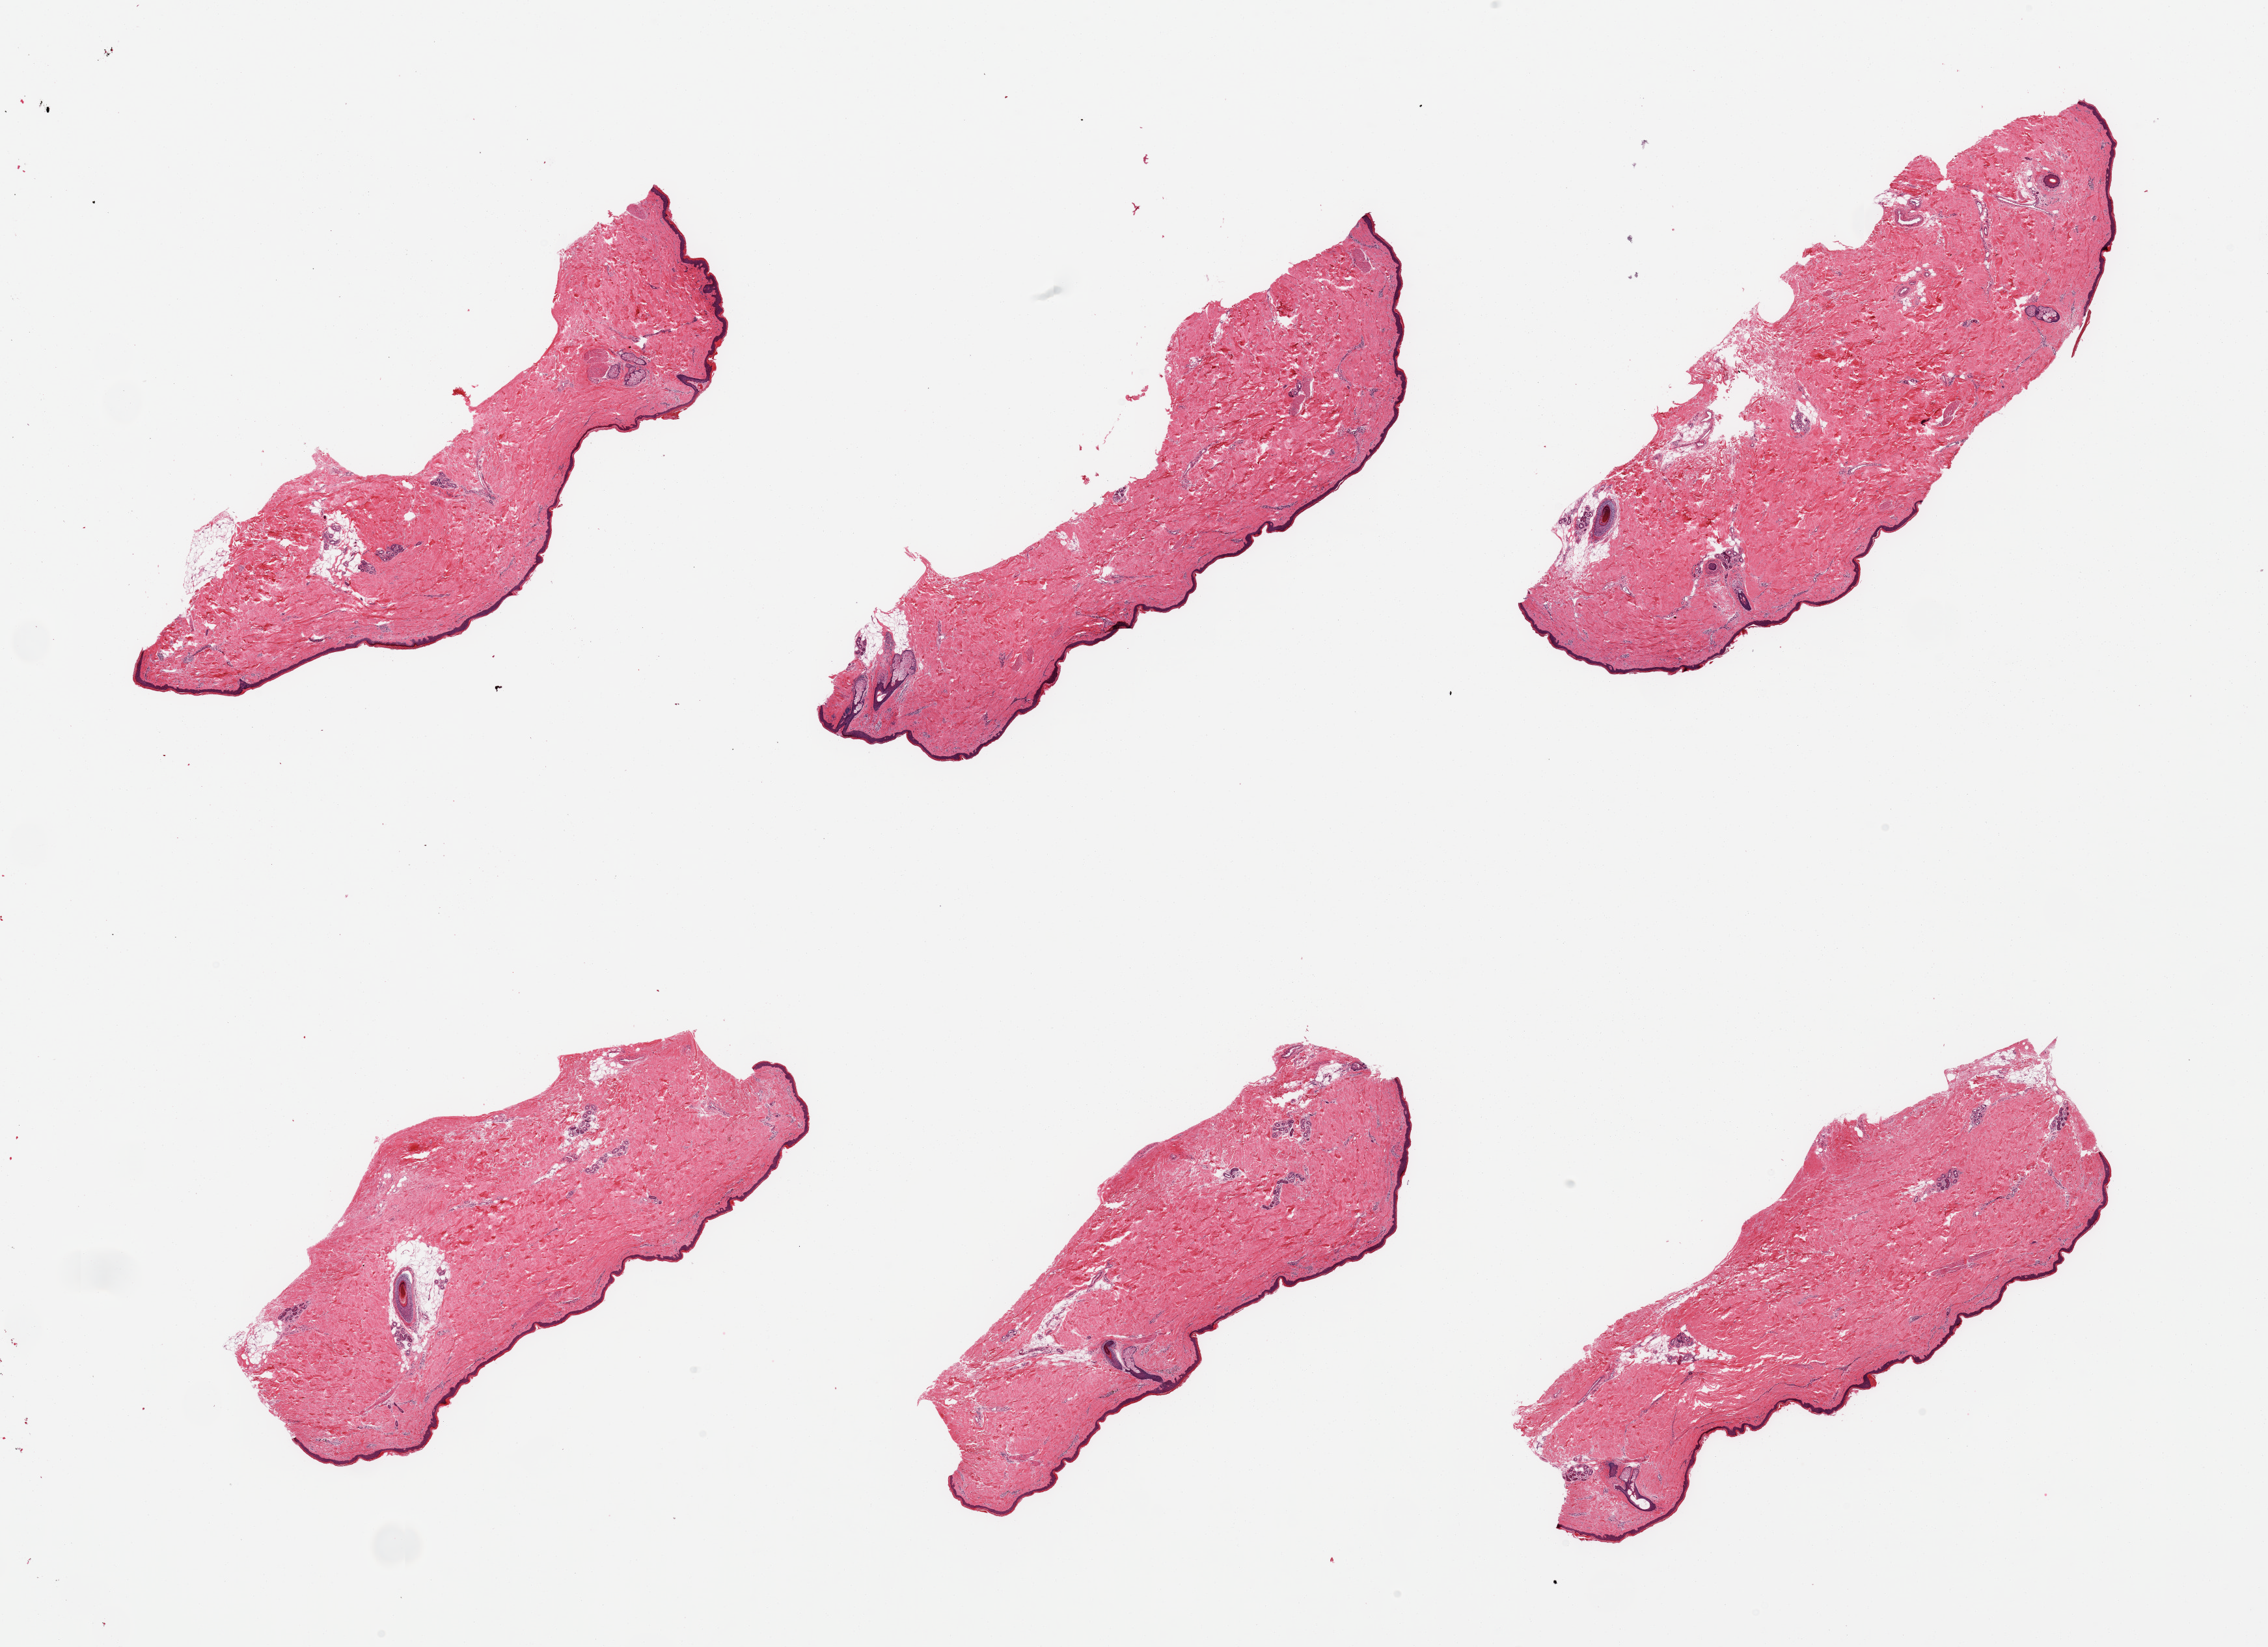
Whole-slide image, H&E stain, whole scanned area (about 27.6 x 20.0 mm, from a 20x scan) shown as a low-resolution overview, PAXgene-fixed, paraffin-embedded tissue, section of skin of lower leg (target tissue), tissue donor sample. Donor: male.
Reviewer comment on this tissue sample: 6 pieces, no dermal fat, squamous epithelium is ~40-50 microns.